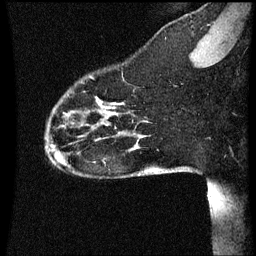
Breast MRI (dynamic contrast-enhanced), one sagittal slice. Slice 13 of 60 in the series (ordered by position). Dynamic contrast-enhanced series, image 2 of 3 at this slice position (ordered by acquisition). 1.5 T. TE 4.2 ms, TR 8.9 ms. 2 mm slice thickness. 256 × 256 image matrix, field of view 200 × 200 mm. Patient: female, 35 years. From the clinical record (not read from this slice): setting: breast cancer imaged before/during neoadjuvant chemotherapy; receptor status: HER2-positive.
Annotated regions visible in this slice (semi-automatically segmented with operator editing):
- analysis volume of interest (the breast-tissue region the enhancement analysis was run in; not a lesion): bounding box [x1, y1, x2, y2] px = [44, 66, 177, 177]
- tumour enhancement mask (voxels above the 70 % enhancement threshold inside the analysis volume of interest): [100, 102, 121, 111]